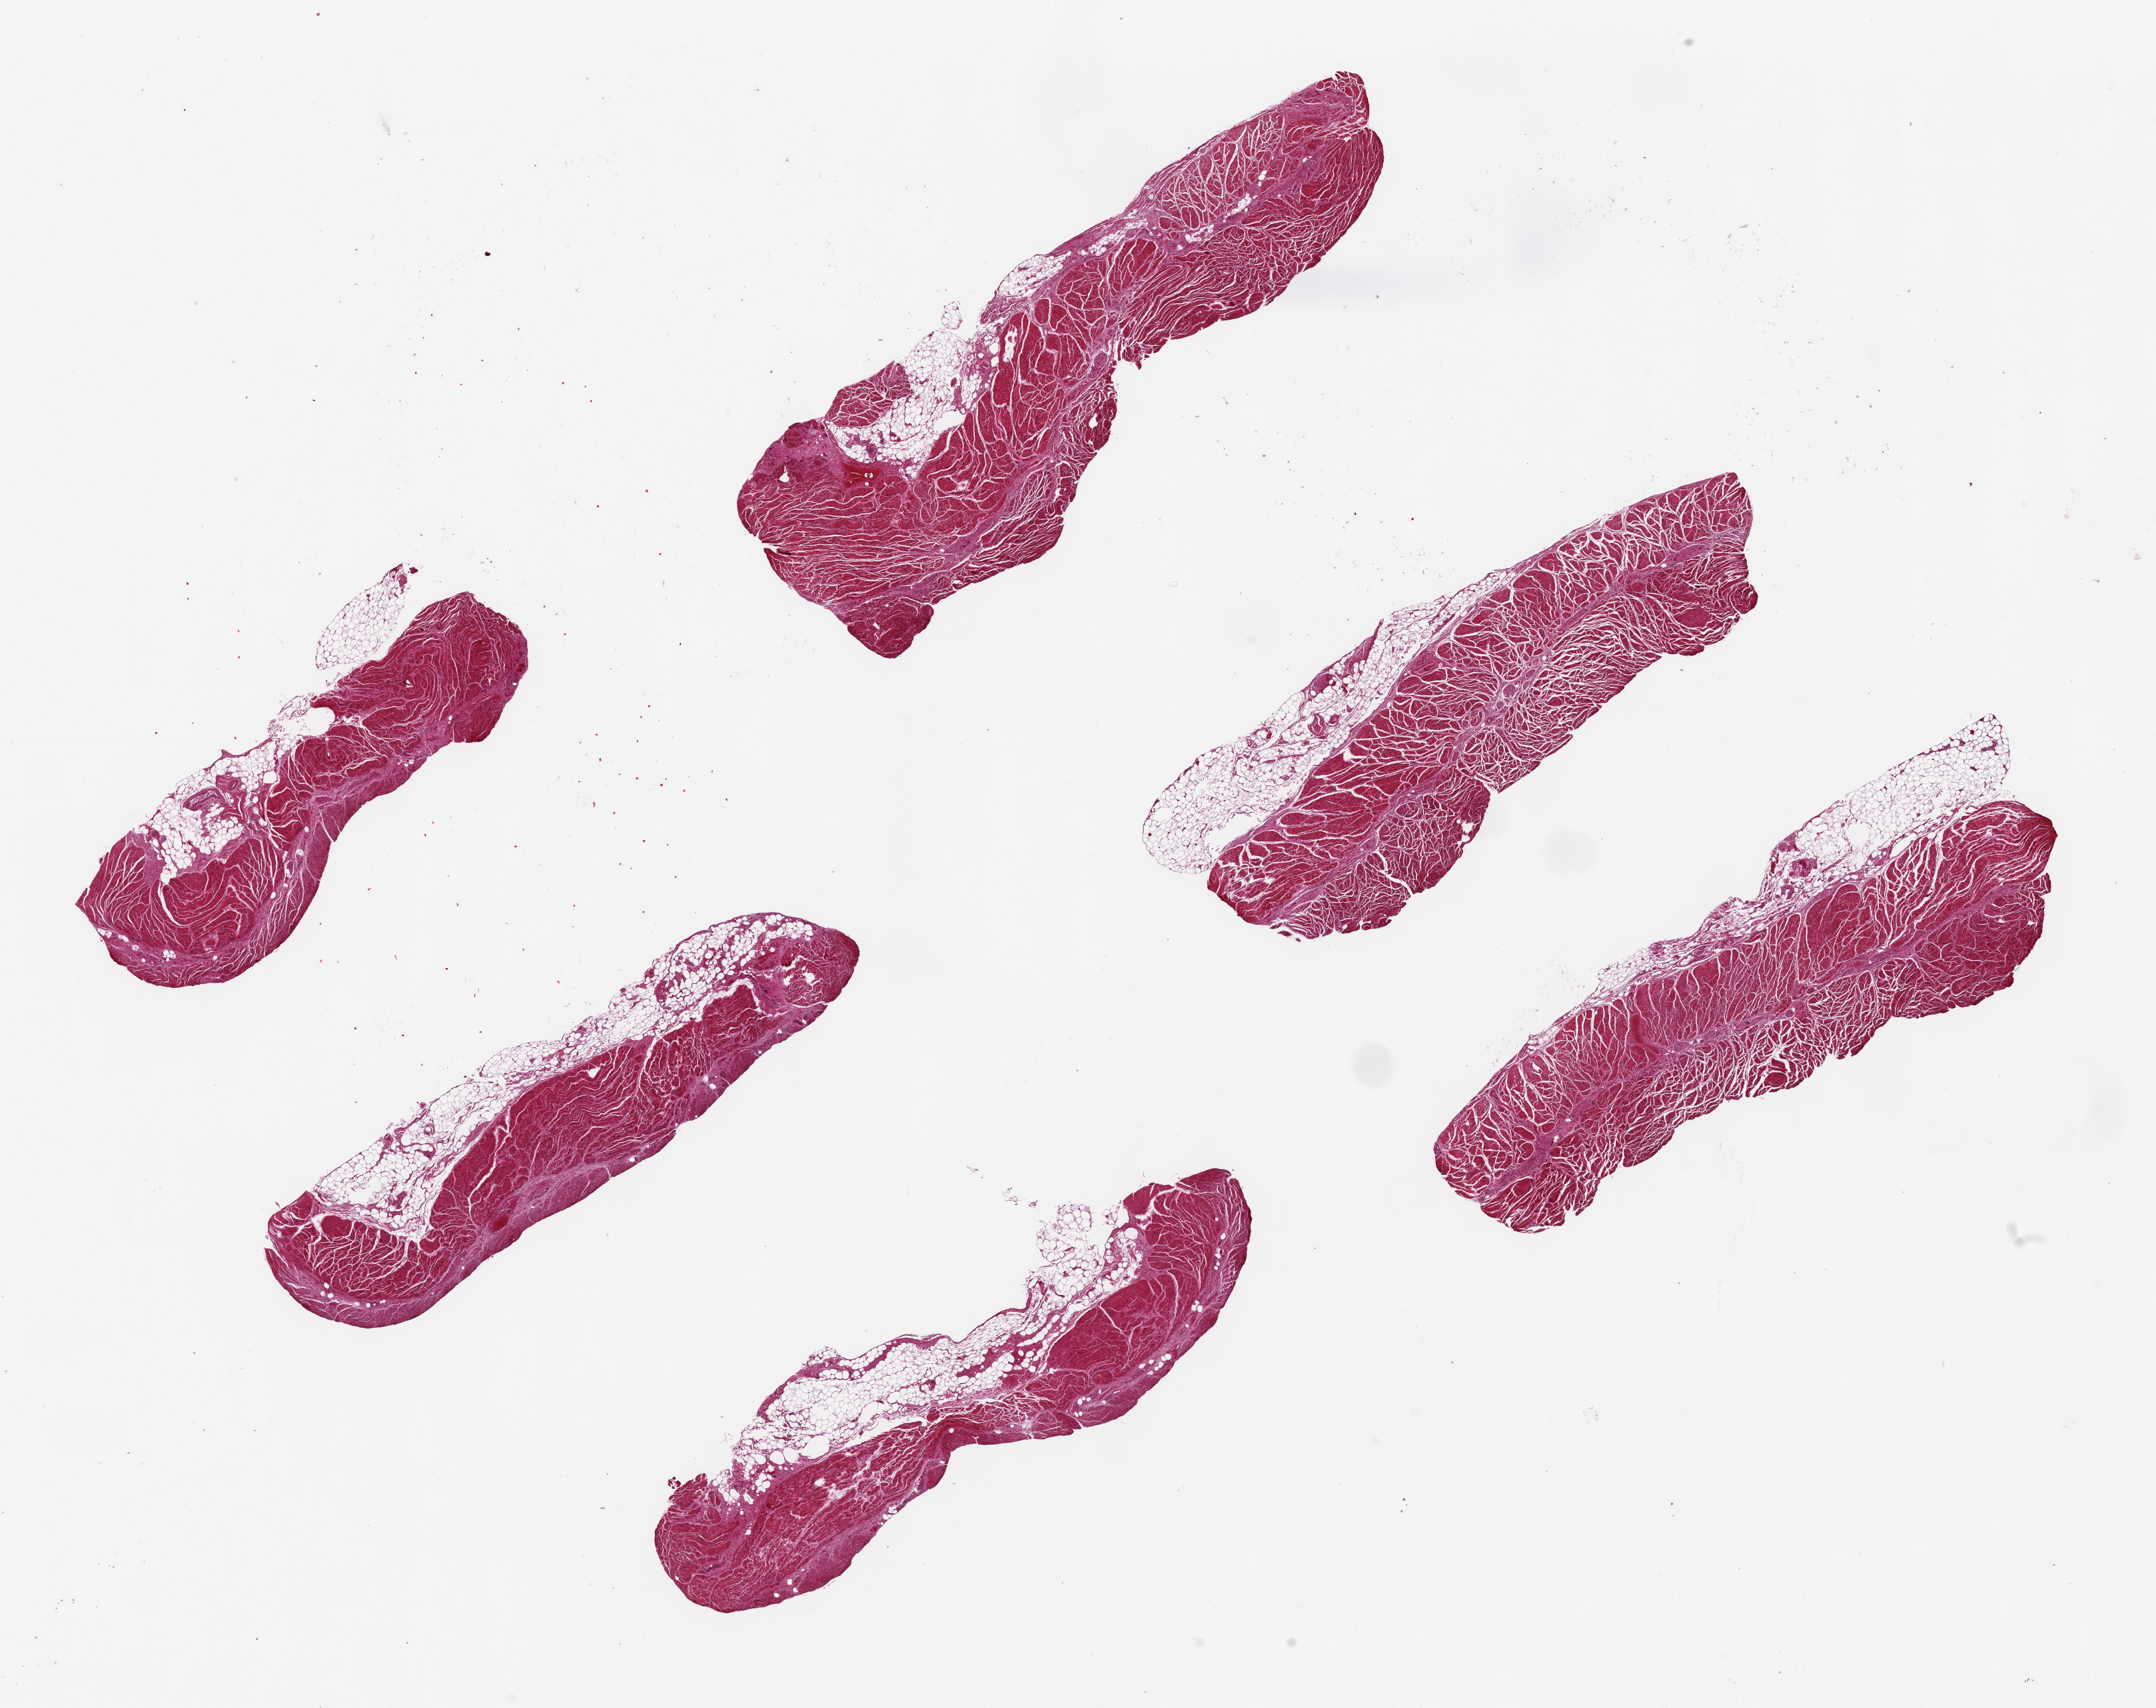
Digitized H&E-stained section, brightfield — whole scanned area (about 25.6 x 20.3 mm) shown as a low-resolution overview. PAXgene-fixed, paraffin-embedded tissue. Section of esophageal muscle (target tissue). Donor tissue sample. Donor sex: female.
• review note (as recorded): 6 pieces, ~8x2mm